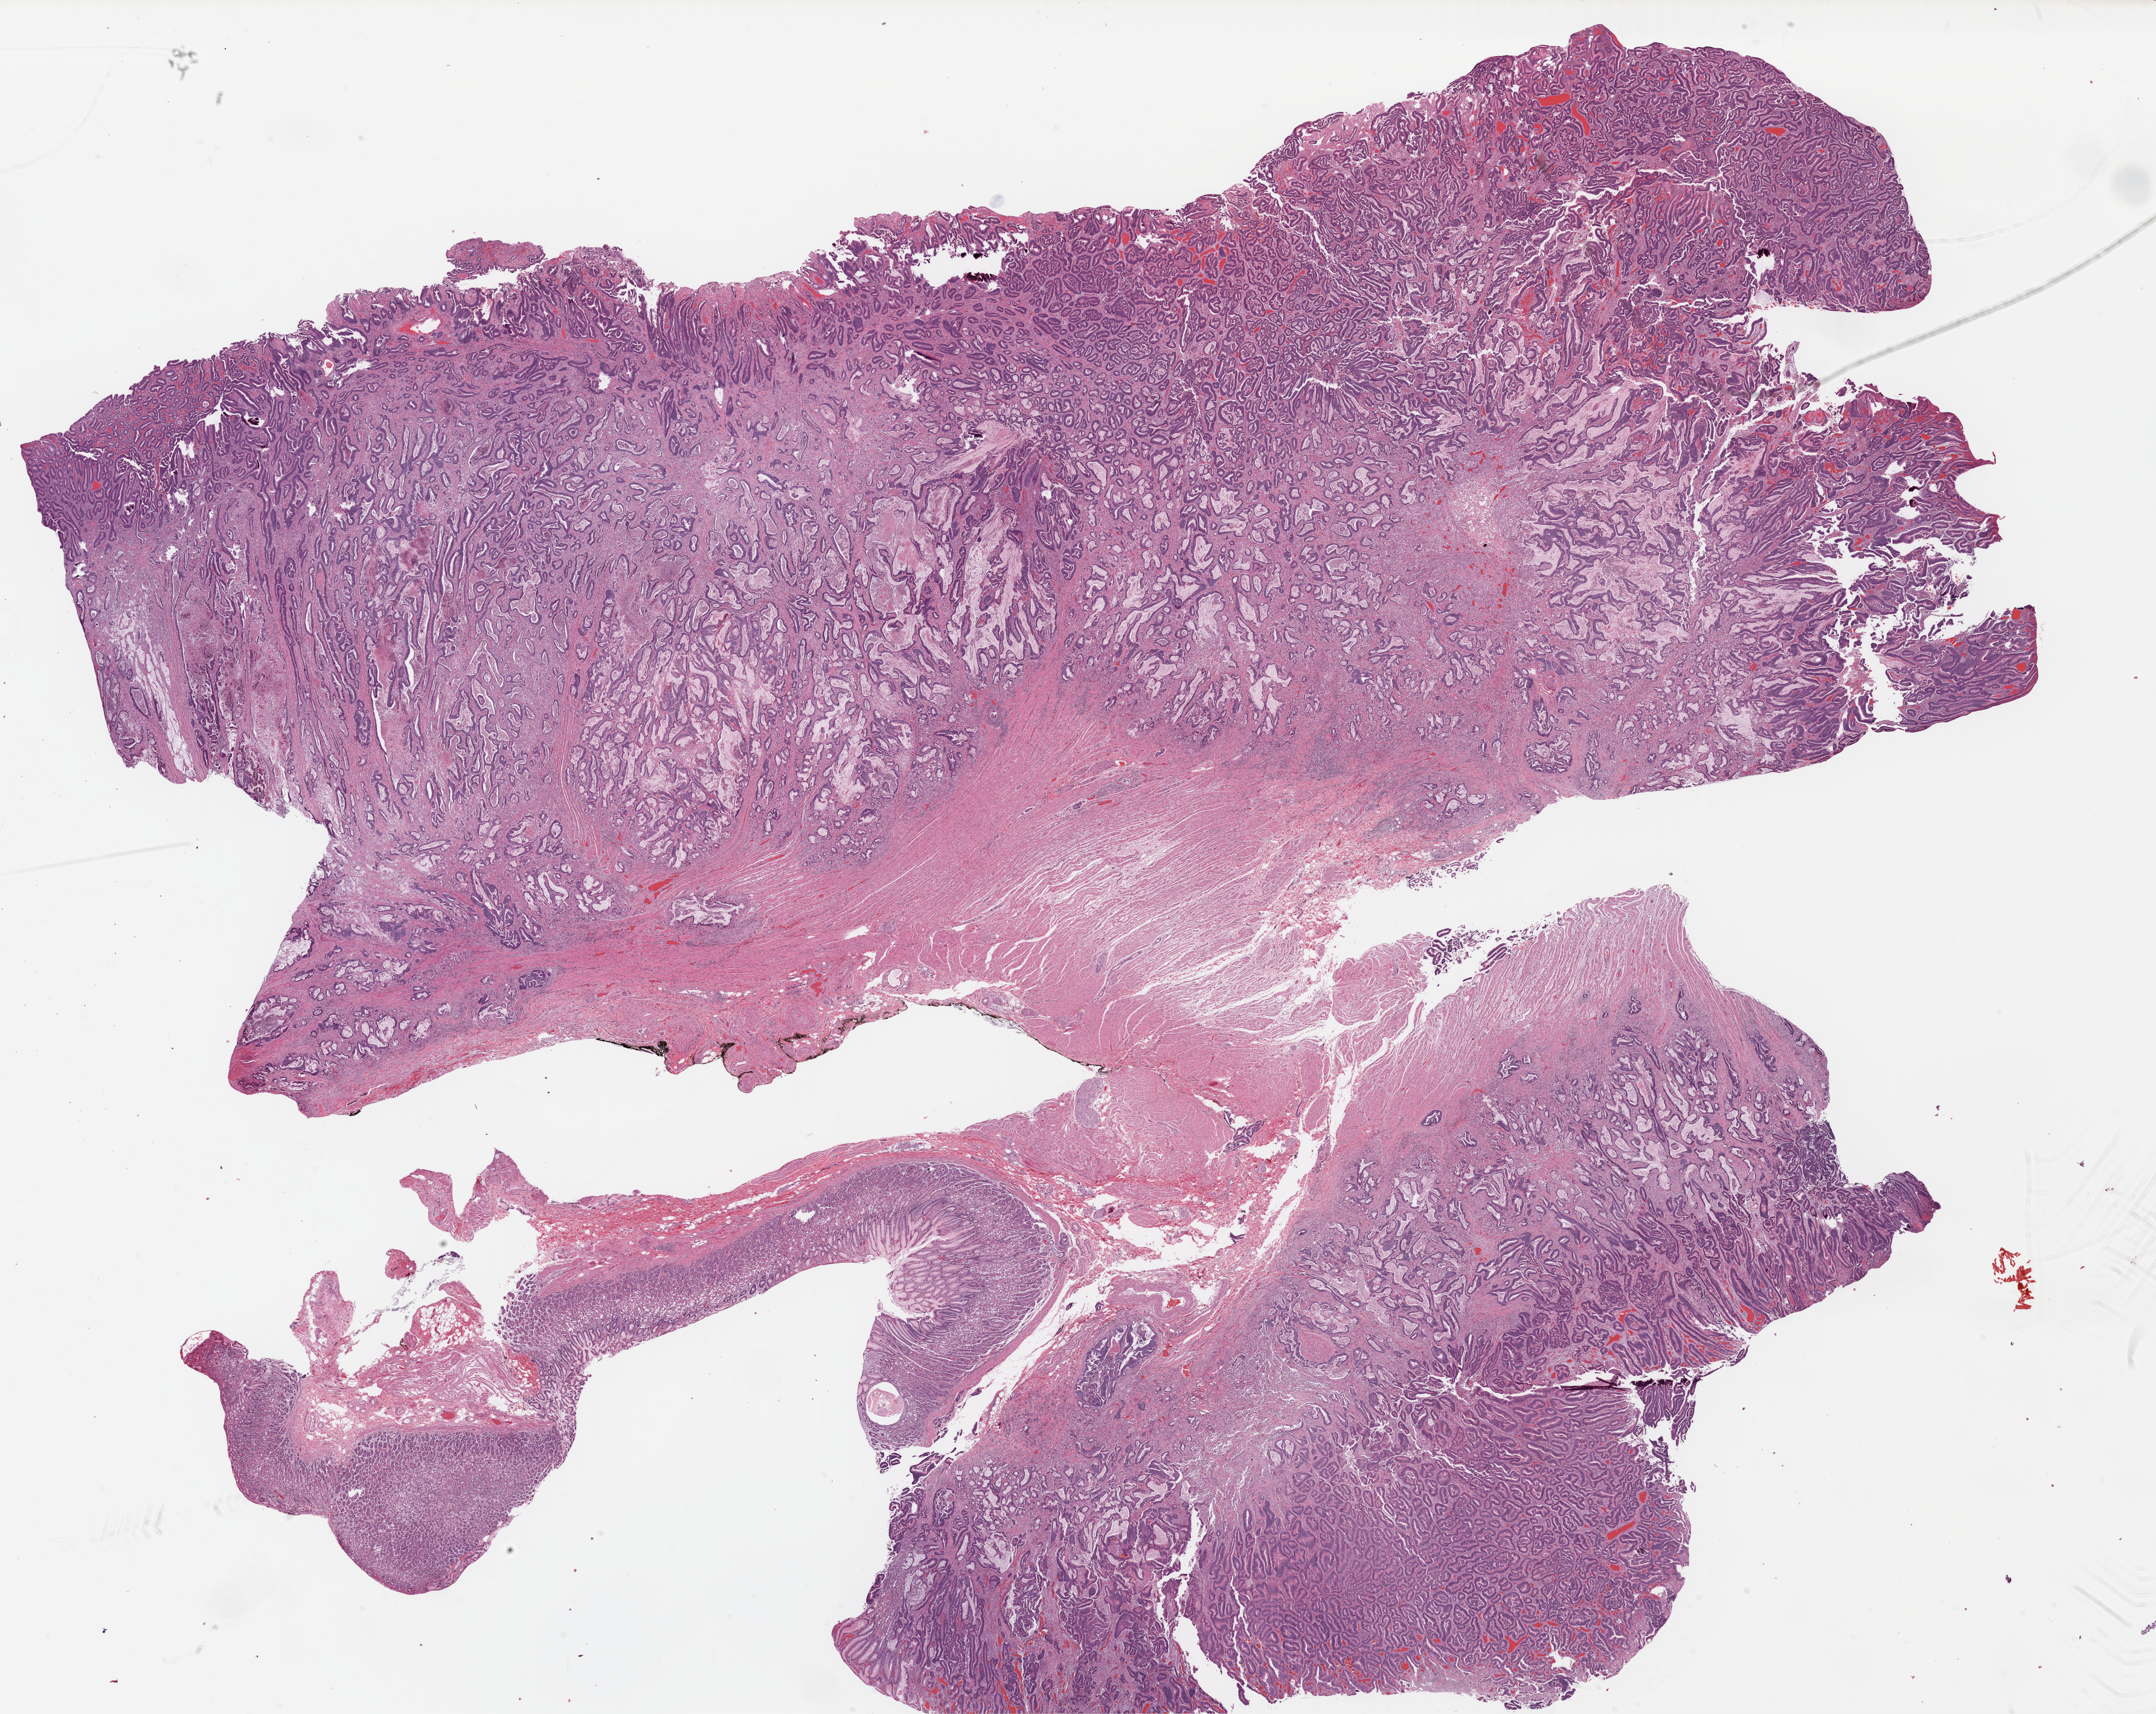
Whole-slide histology image, Hematoxylin and eosin (H&E) stained — shown as a low-resolution overview of the whole scanned area (about 28.1 x 22.3 mm, acquisition: 40x scan). Formalin-fixed paraffin-embedded (FFPE) diagnostic section. Primary tumour sample from the esophagus. Male, age 79 years at initial diagnosis. Histologic grade: G2 (moderately differentiated).
AJCC pathologic stage: IIIC (7th edition). Diagnosis: Adenocarcinoma, NOS (lower third of esophagus).